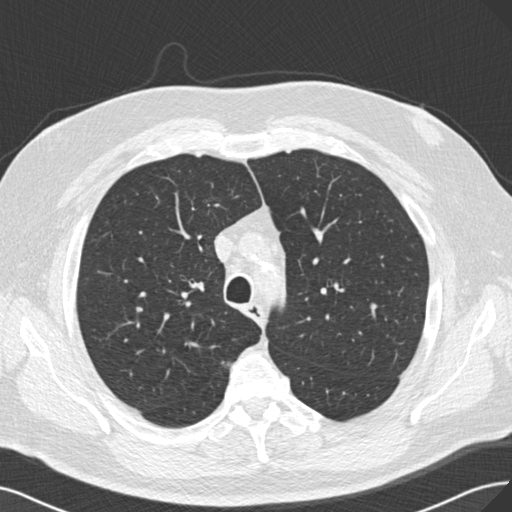
Low-dose screening chest CT, axial slice, baseline screening round, lung window (W 1500 / L -600 HU), 2 mm slice thickness, standard (soft-tissue) reconstruction kernel (B30f), 120 kVp. Male, age 67 years at enrolment. Current smoker at enrolment.
• Expert reader's lesion annotation, box from (x=130, y=300) to (x=146, y=318) px.
• Screening reader's record for this exam: no non-calcified nodule ≥4 mm recorded.
• Official screen result: negative screen, minor abnormalities not suspicious for lung cancer.